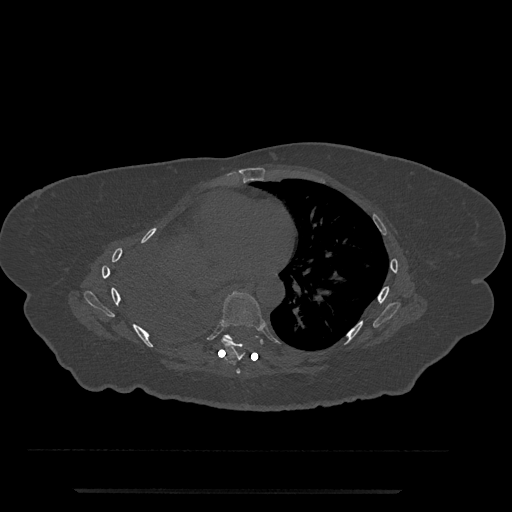
CT including the spine, one axial slice. Position 430 of 797 along the scan axis. Reconstruction kernel Br40s/3. Bone window (W 1800 / L 400 HU). 512 × 512 image matrix. Female patient, age 51 years. From the clinical record (not read from this slice): primary cancer: neuro; vertebrae with lytic lesions (as recorded): T8.
Structures marked on this image (semi-automatically segmented with operator editing):
- T6 vertebra: box from (x=236, y=369) to (x=241, y=374) px
- T7 vertebra: (x=221, y=291)–(x=264, y=360)
- T8 vertebra: (x=223, y=334)–(x=233, y=340)